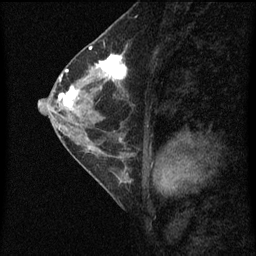
Breast MRI (dynamic contrast-enhanced), one sagittal slice. Slice 32 of 60 in the series (ordered by position). Dynamic contrast-enhanced series, image 2 of 4 at this slice position (ordered by acquisition). 1.5 T. TE 4.2 ms, TR 8 ms. 2 mm slice thickness. 256 × 256 image matrix, field of view 180 × 180 mm. Female patient, age 56 years.
Annotated regions visible in this slice (semi-automatic segmentation, software-assisted and operator-edited):
- analysis volume of interest (the breast-tissue region the enhancement analysis was run in; not a lesion): box from (x=56, y=52) to (x=129, y=115) px
- tumour enhancement mask (voxels above the 70 % enhancement threshold inside the analysis volume of interest): (x=58, y=54)–(x=128, y=109)